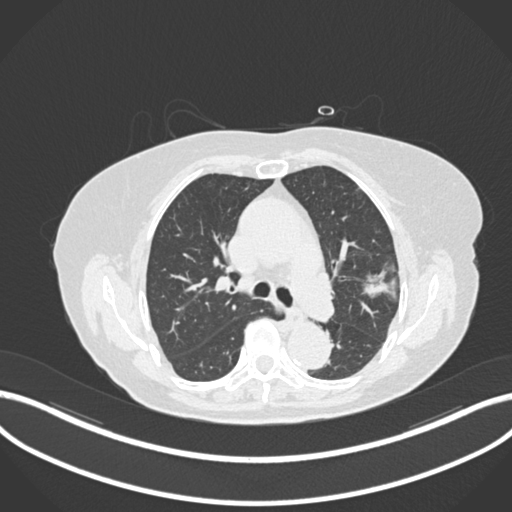
Chest CT, one axial slice; slice 103 of 168 in the series (ordered by position); reconstruction kernel B30f; lung window (W 1500 / L -600 HU); 1 mm slice thickness; 512 × 512 image matrix, field of view 400 × 400 mm. Patient: female, 75 years. Case-level facts recorded for this patient, not image findings: clinical TNM (as recorded): T1c N0 M0.
Structures marked on this image (bounding box drawn by a radiologist):
- lung tumour (recorded histology: adenocarcinoma): box from (x=361, y=266) to (x=387, y=301) px